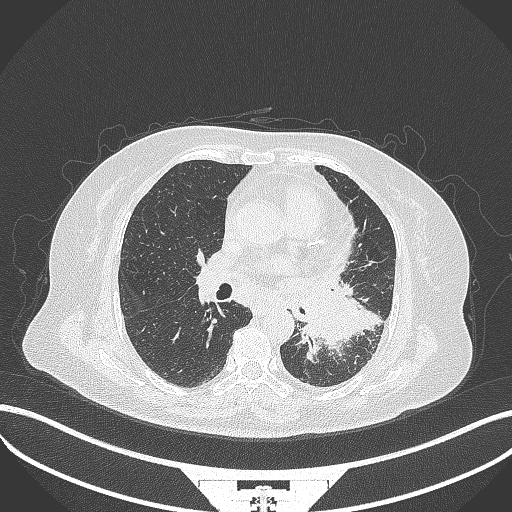
Chest CT, one axial slice. Slice 182 of 322 in the series (ordered by position). Reconstruction kernel B70f. Lung window (W 1500 / L -600 HU). 512 × 512 image matrix. Patient: female, 69 years. Case-level facts recorded for this patient, not image findings: clinical TNM (as recorded): T2b N3 M1.
Outlined on this slice (rectangle marked by the reading radiologist):
- lung tumour (recorded histology: adenocarcinoma): bounding box <297,282,371,355> (left, top, right, bottom; pixels)